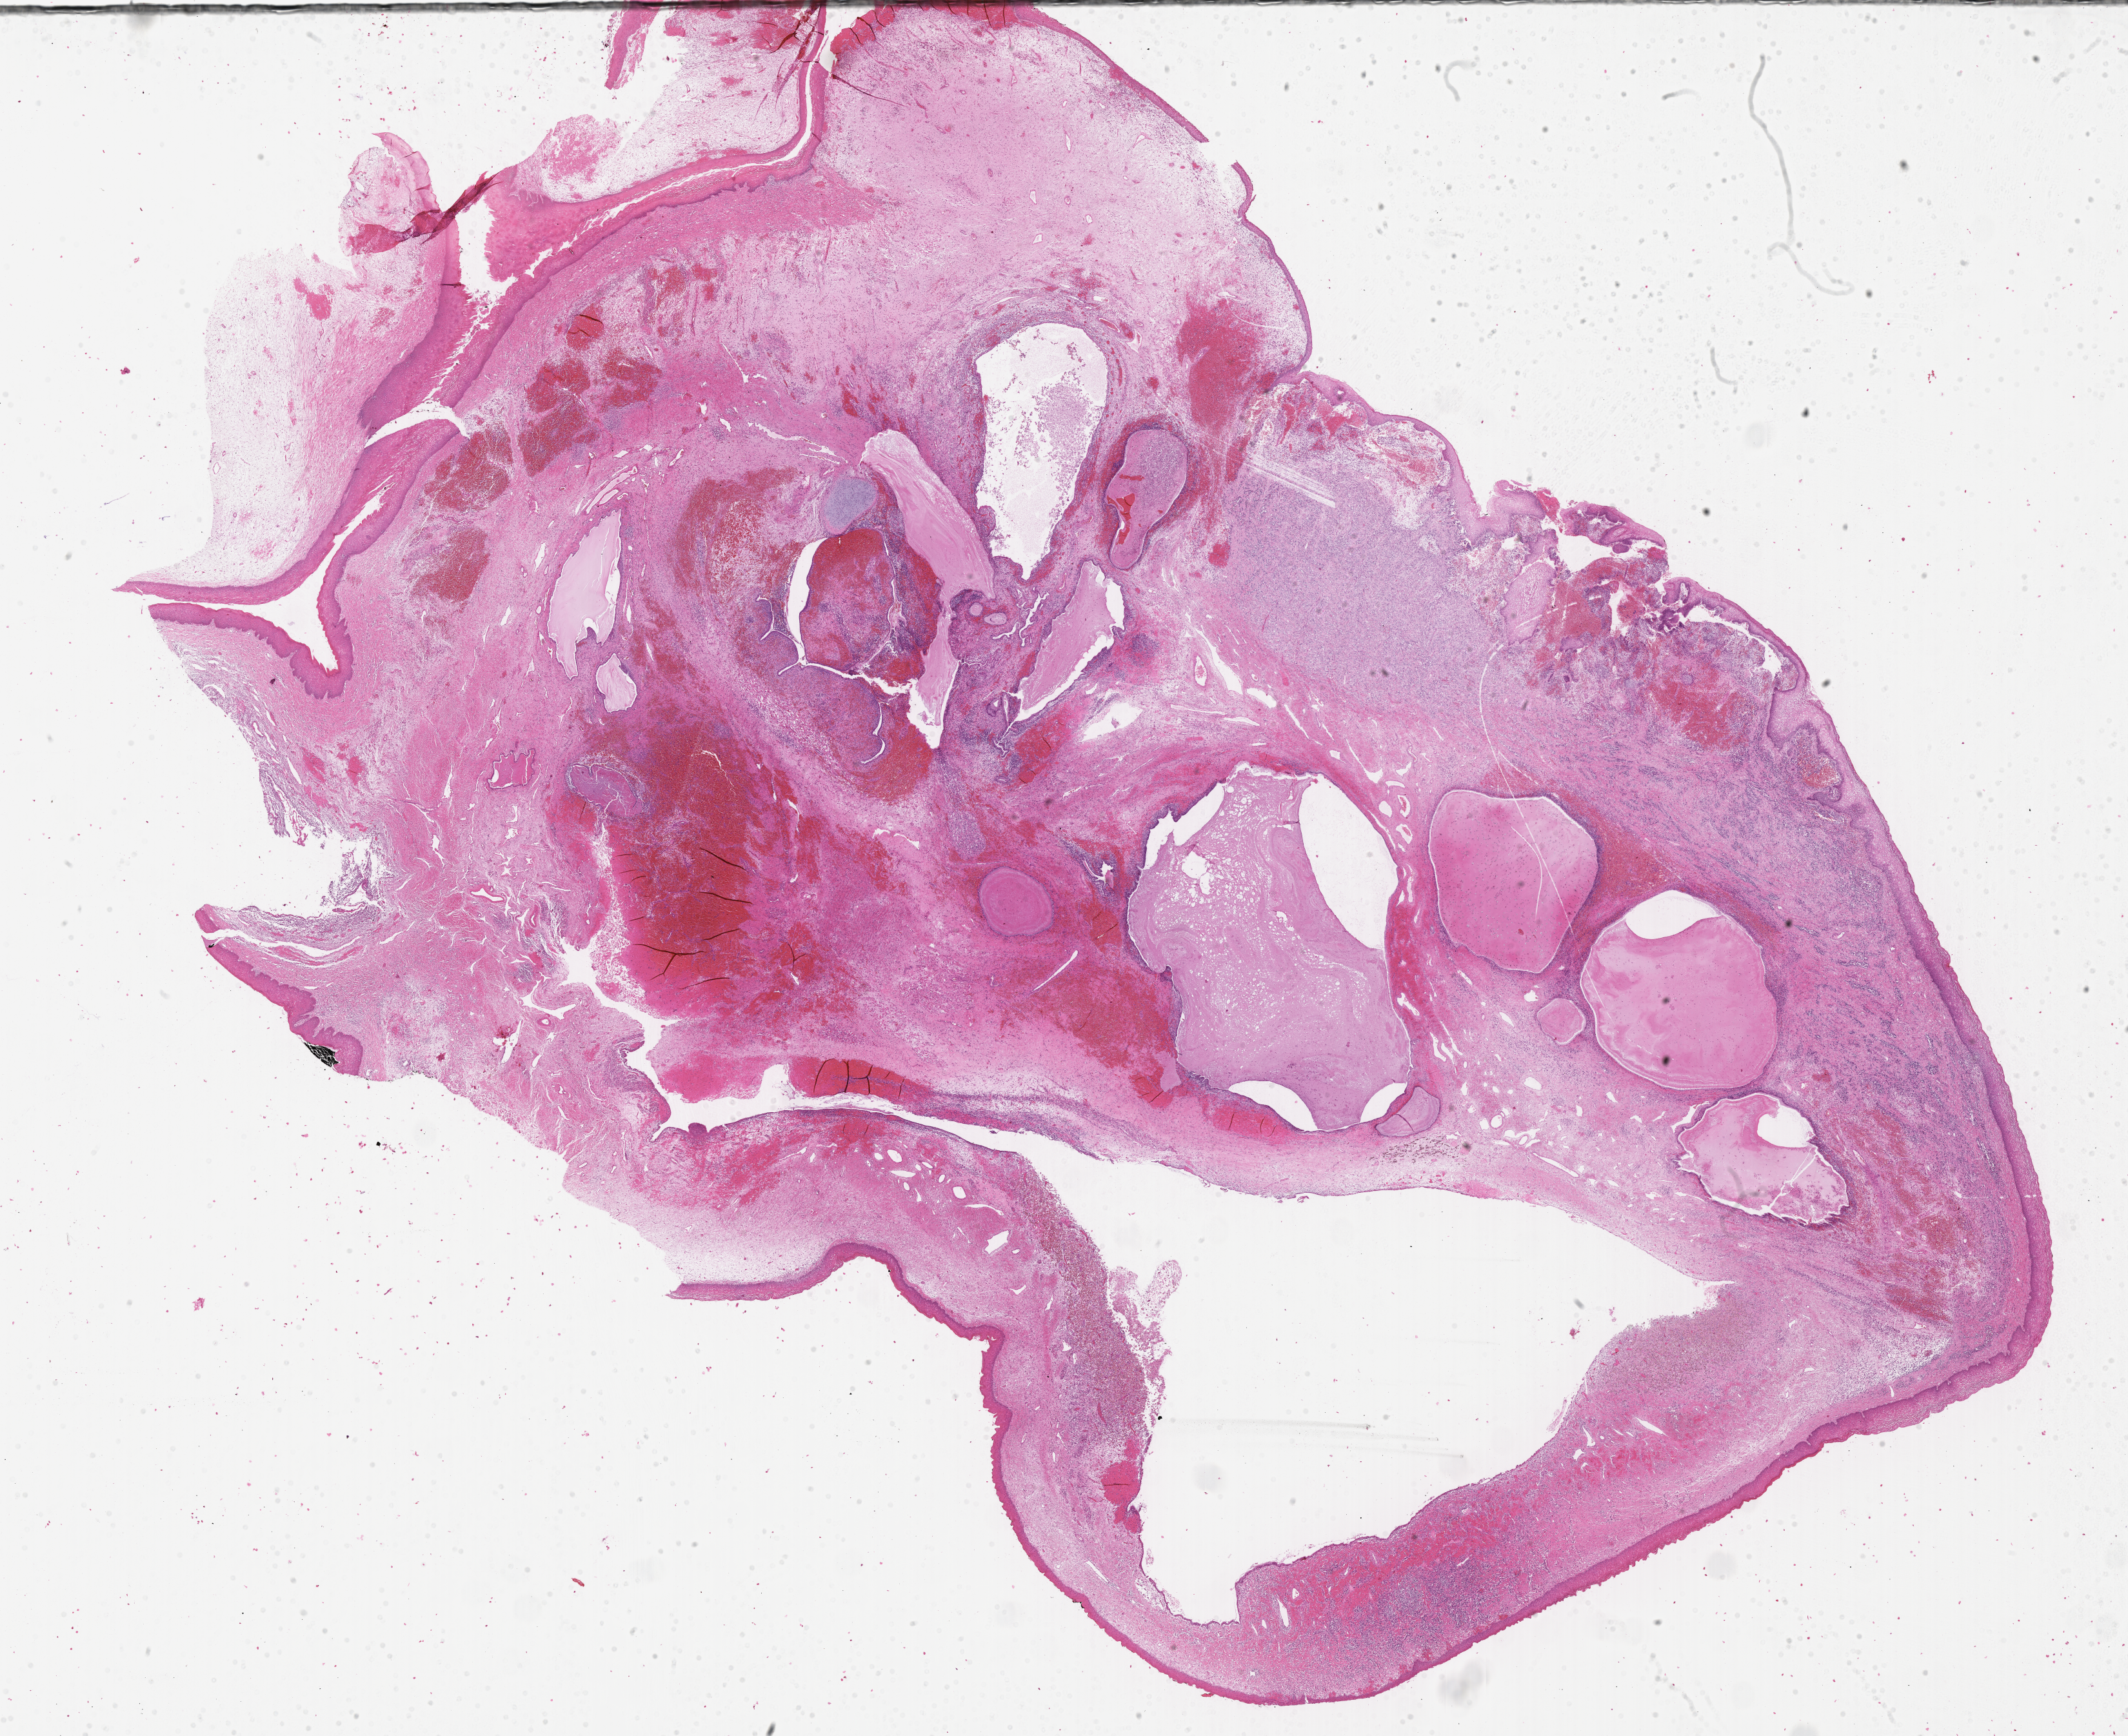
Hematoxylin and eosin (H&E) whole-slide image of tumor tissue, low-resolution overview of the scanned area, about 26.7 x 21.8 mm. FFPE section. Sample anatomic site: cervix. Patient: female, age 18.1 years at diagnosis.
- stage (as recorded): 1
- diagnosis: rhabdomyosarcoma; histological classification: embryonal rhabdomyosarcoma